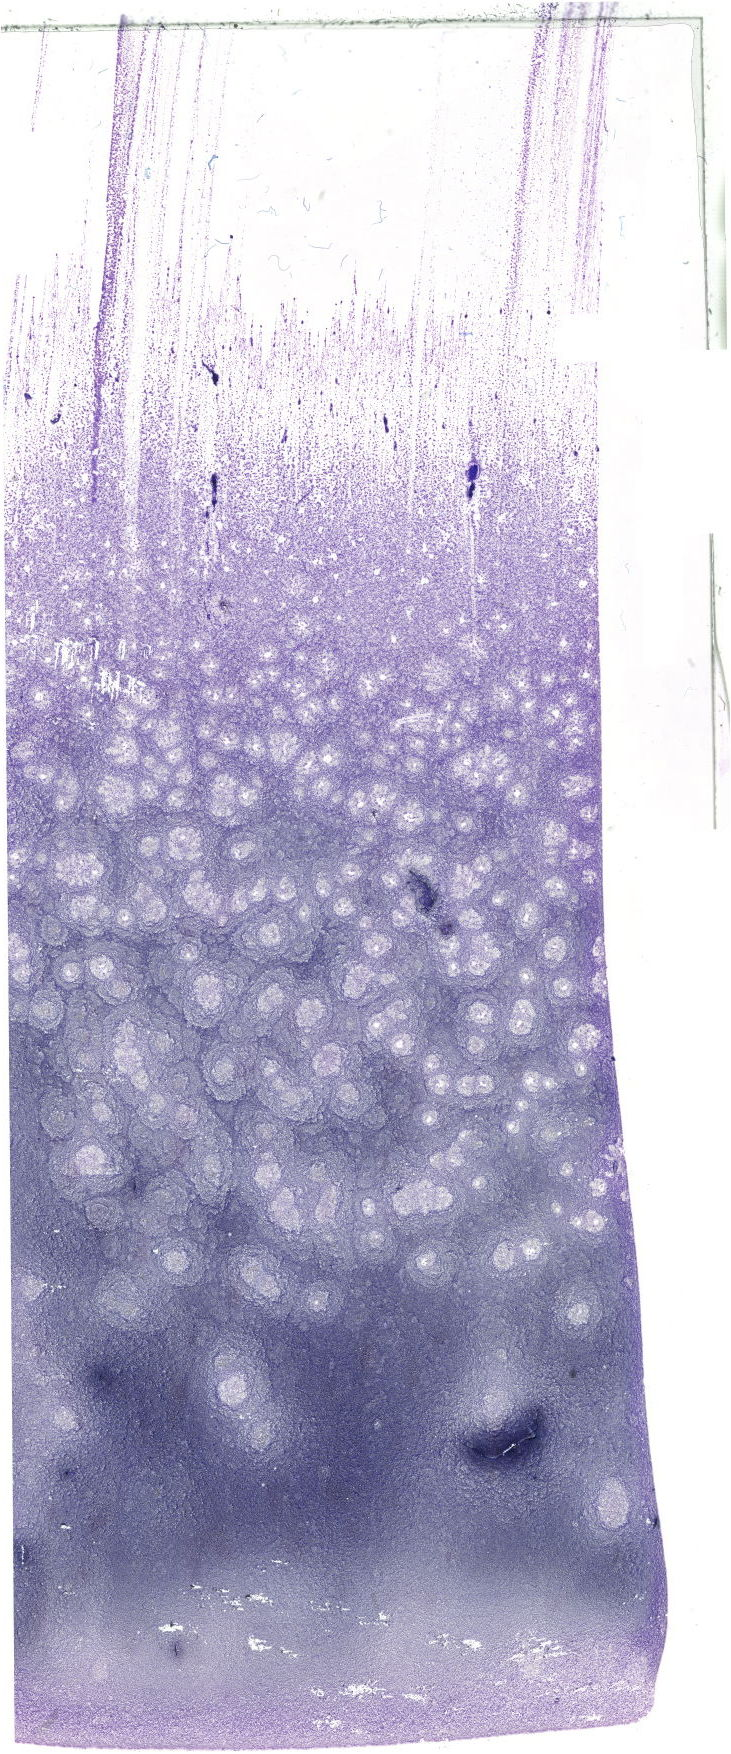
May-Grünwald-Giemsa (MGG)-stained marrow aspirate smear (whole slide) — low-resolution overview of the scanned area, about 20.7 x 49.7 mm. Patient sex: female.
Diagnosis: Chronic Phase Chronic Myeloid Leukemia, BCR-ABL1 Positive.